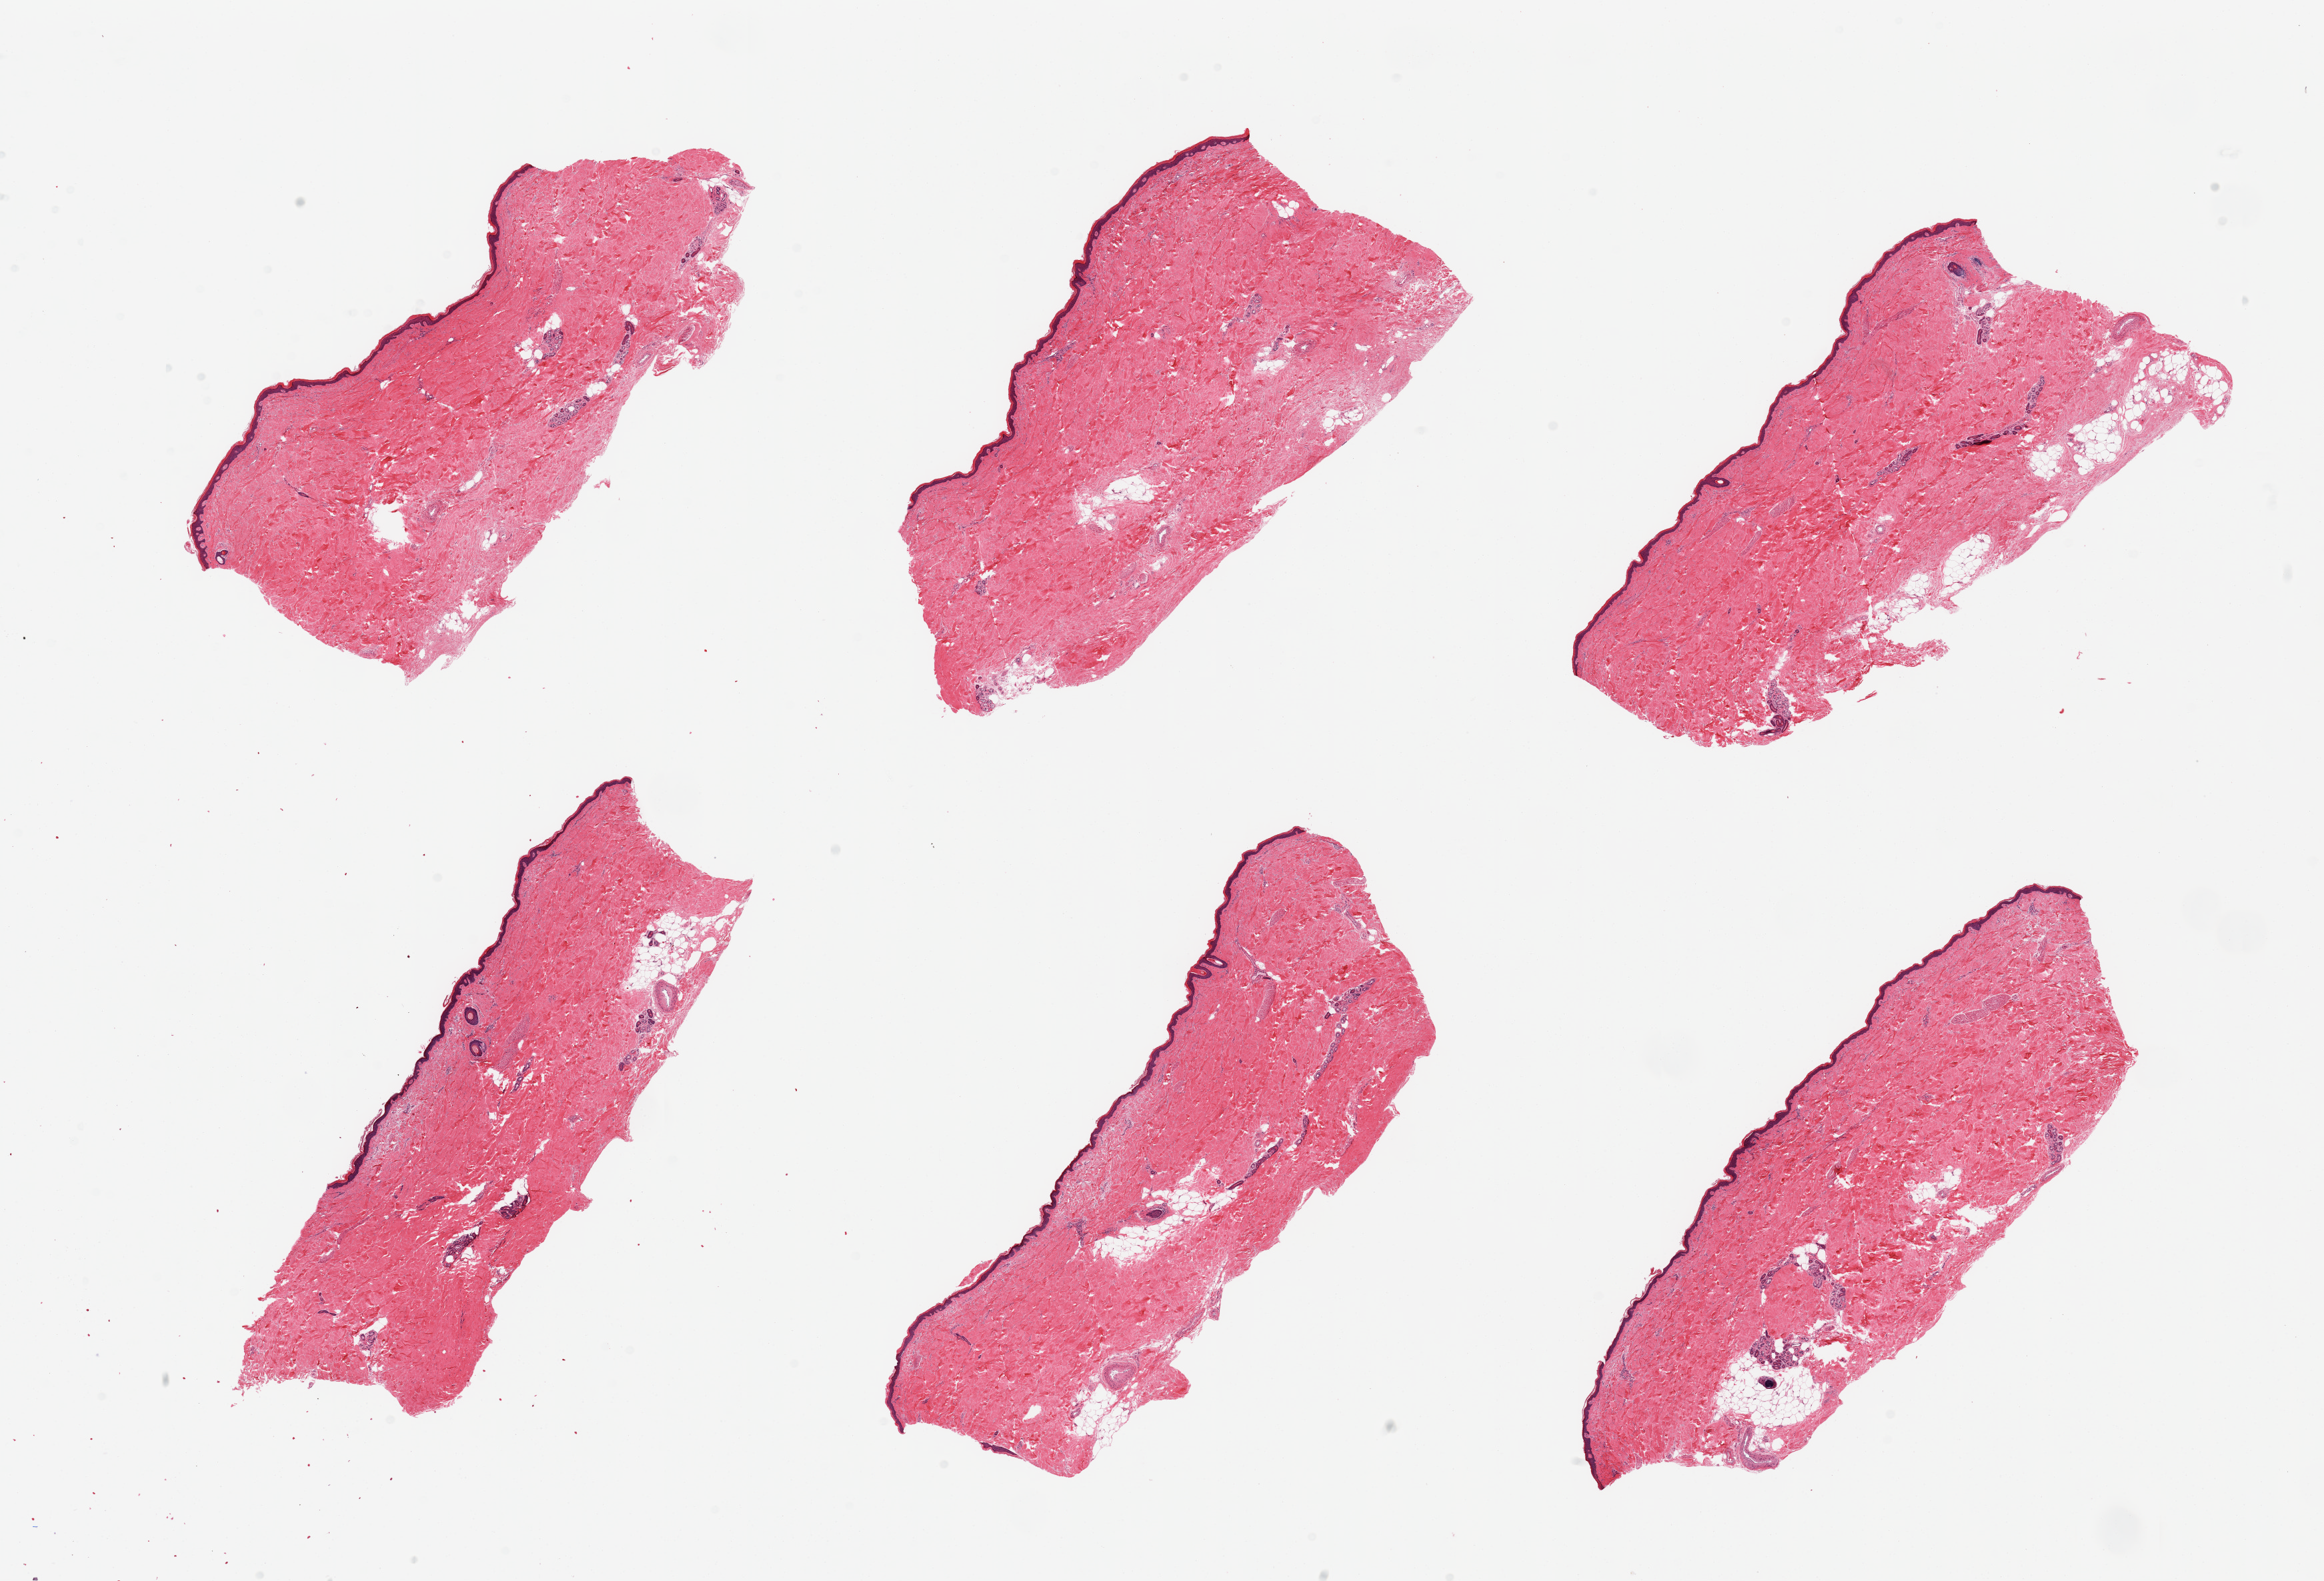
H&E whole-slide image, whole scanned area (about 27.6 x 18.8 mm) shown as a low-resolution overview; PAXgene-fixed paraffin-embedded (PFPE) section; sampled site (target tissue): skin of lower leg; donor tissue sample. Donor sex: male.
Reviewer comment on this tissue sample: 6 pieces; ~10% external/periadnexal fat; 49um epidermis.